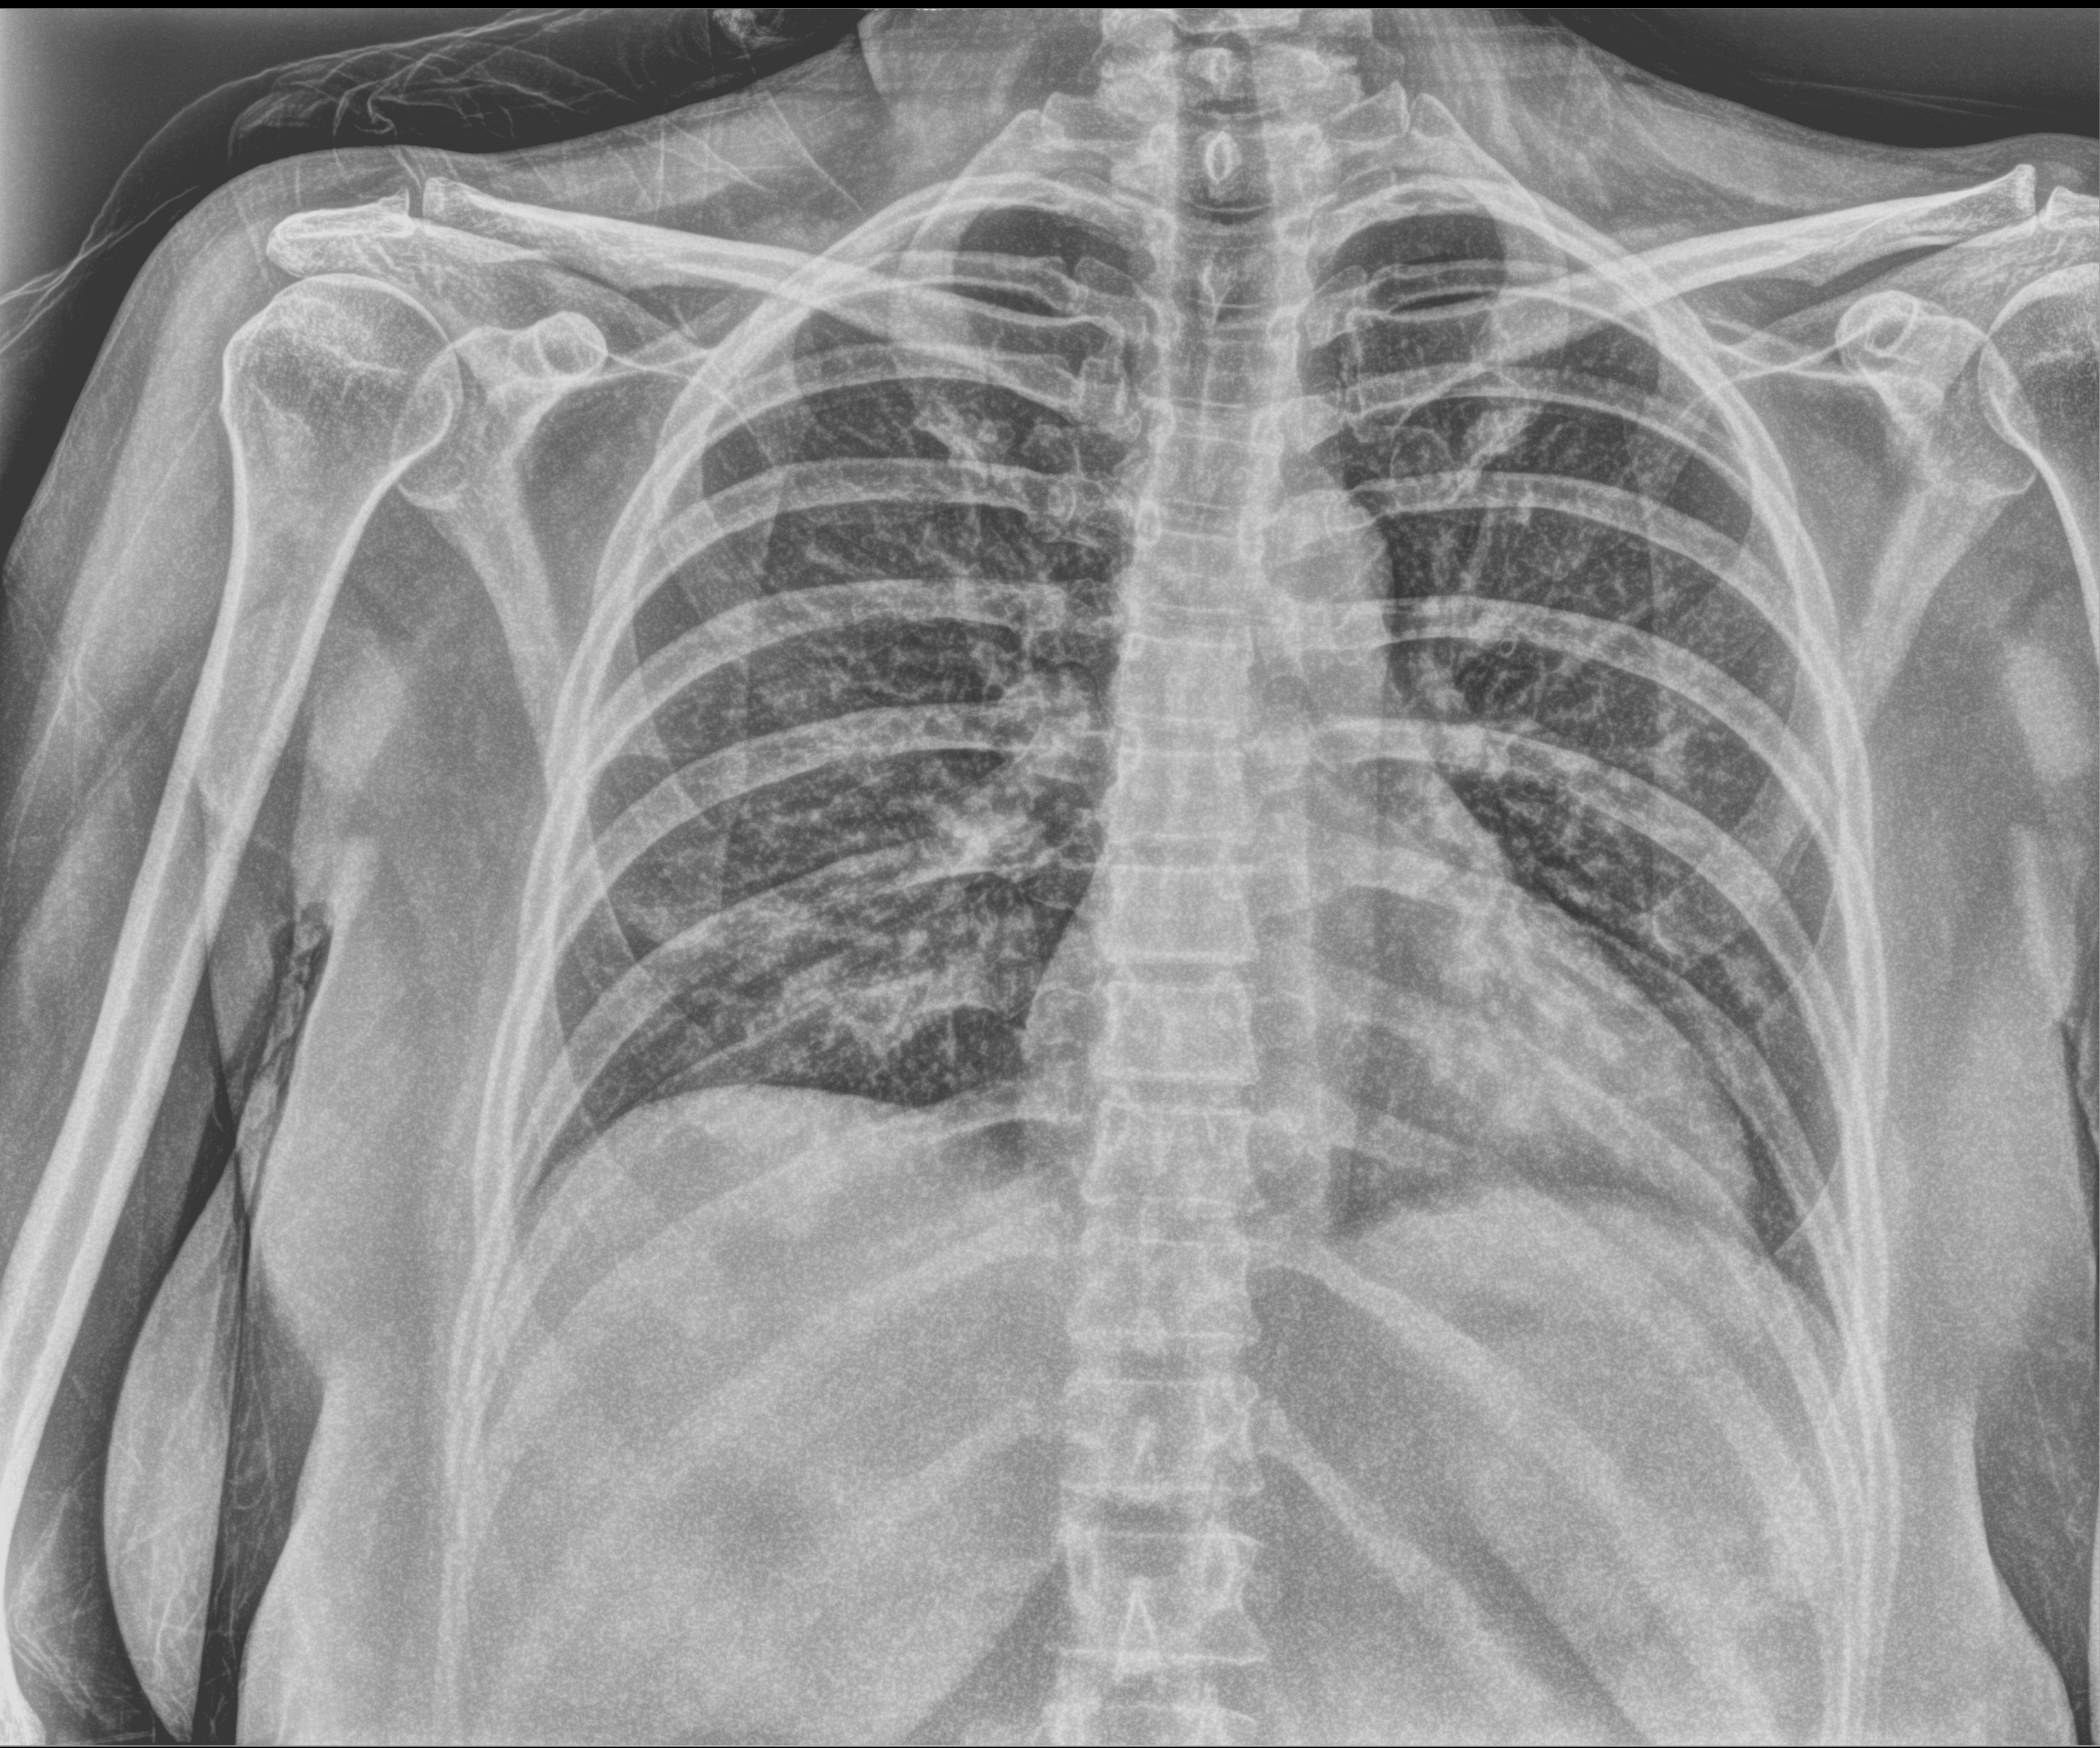
Bedside chest radiograph (computed radiography), anteroposterior (AP) projection. Patient hospitalised with COVID-19; female, aged 18–59 years.
Hospital-stay facts (about this admission, not read from this image; timing relative to this image not recorded): admitted to intensive care during this hospital stay: no.